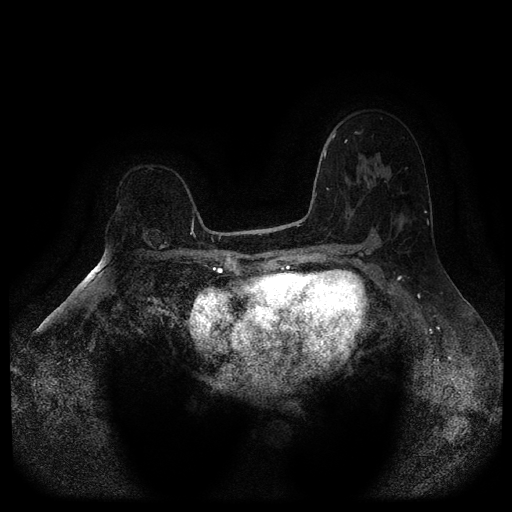
Breast MRI (dynamic contrast-enhanced, multi-phase), one axial slice. Position 68 of 116 along the scan axis. Dynamic contrast-enhanced series, time point 2 of 5 at this slice position (early post-contrast). 1.5 T. TE 2.6 ms, TR 5.4 ms. 2 mm slice thickness. 512 × 512 image matrix, field of view 340 × 340 mm. Patient: female, 64 years.
Outlined on this slice (semi-automatically segmented with operator editing):
- breast lesion (labelled benign in the annotation): box from (x=141, y=227) to (x=171, y=252) px